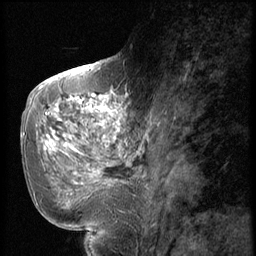
Breast MRI (dynamic contrast-enhanced), one sagittal slice; position 27 of 56 along the scan axis; dynamic contrast-enhanced series, image 2 of 2 at this slice position (ordered by acquisition); 1.5 T; TE 4.2 ms, TR 9 ms; 2.5 mm slice thickness; 256 × 256 image matrix. Female patient, age 51 years. From the clinical record (not read from this slice): setting: breast cancer imaged before/during neoadjuvant chemotherapy; receptor status: triple-negative.
Outlined on this slice (semi-automatically segmented with operator editing):
- analysis volume of interest (the breast-tissue region the enhancement analysis was run in; not a lesion): box from (x=60, y=98) to (x=147, y=197) px
- tumour enhancement mask (voxels above the 140 % enhancement threshold inside the analysis volume of interest): (x=66, y=98)–(x=121, y=175)